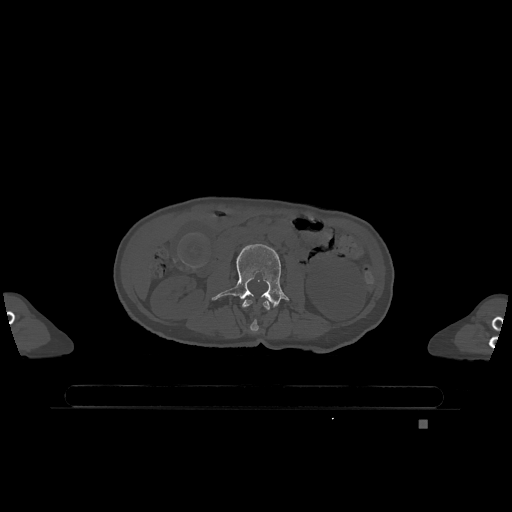
CT including the spine, one axial slice. Slice 367 of 1317 in the series (ordered by position). Bone window (W 1800 / L 400 HU). 0.5 mm slice thickness. 512 × 512 image matrix, field of view 500 × 500 mm. Patient: female, 74 years. Case-level facts recorded for this patient, not image findings: primary cancer: lung.
Annotated regions visible in this slice (semi-automatic segmentation, software-assisted and operator-edited):
- L2 vertebra: box from (x=242, y=299) to (x=270, y=332) px
- L3 vertebra: (x=212, y=244)–(x=289, y=308)